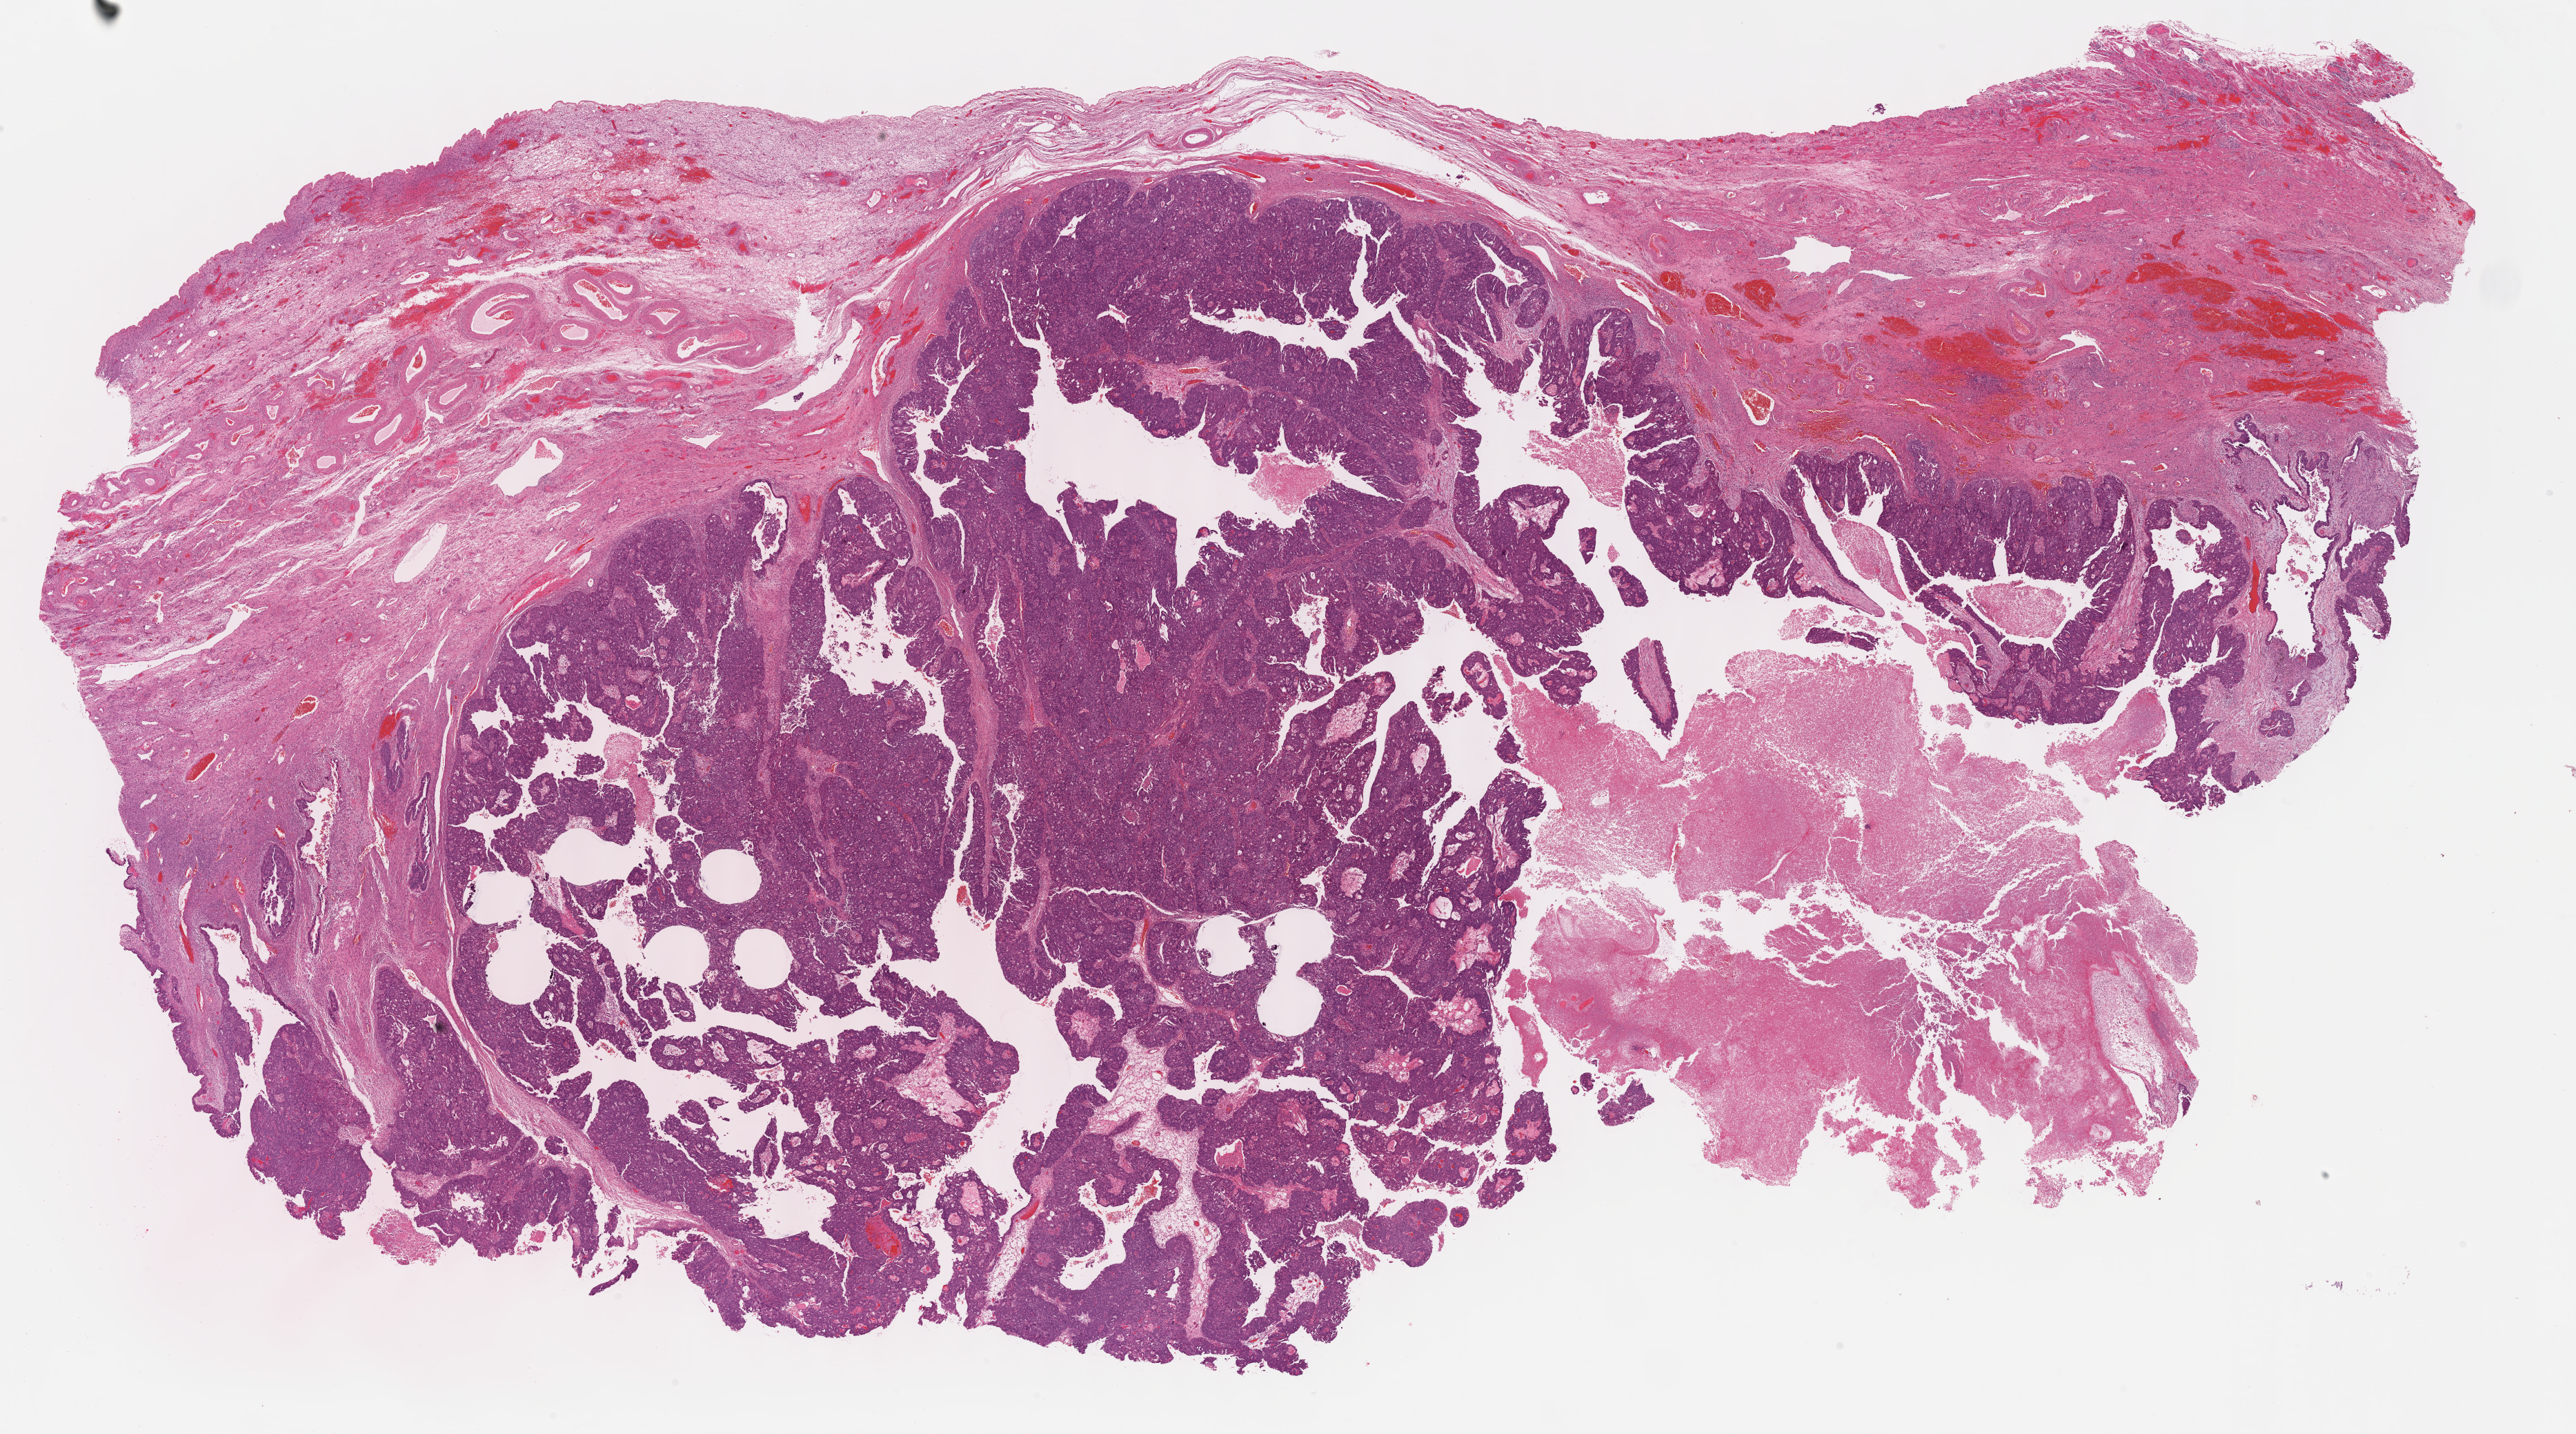
Hematoxylin and eosin (H&E) stained whole-slide image, whole scanned area (about 30.2 x 16.8 mm) shown as a low-resolution overview; formalin-fixed paraffin-embedded (FFPE) diagnostic section; primary tumour sample from the ovary. Patient: female, age at initial diagnosis 65 years. Histologic grade: G3 (poorly differentiated).
FIGO stage: IIIC. Diagnosis: Serous cystadenocarcinoma, NOS.